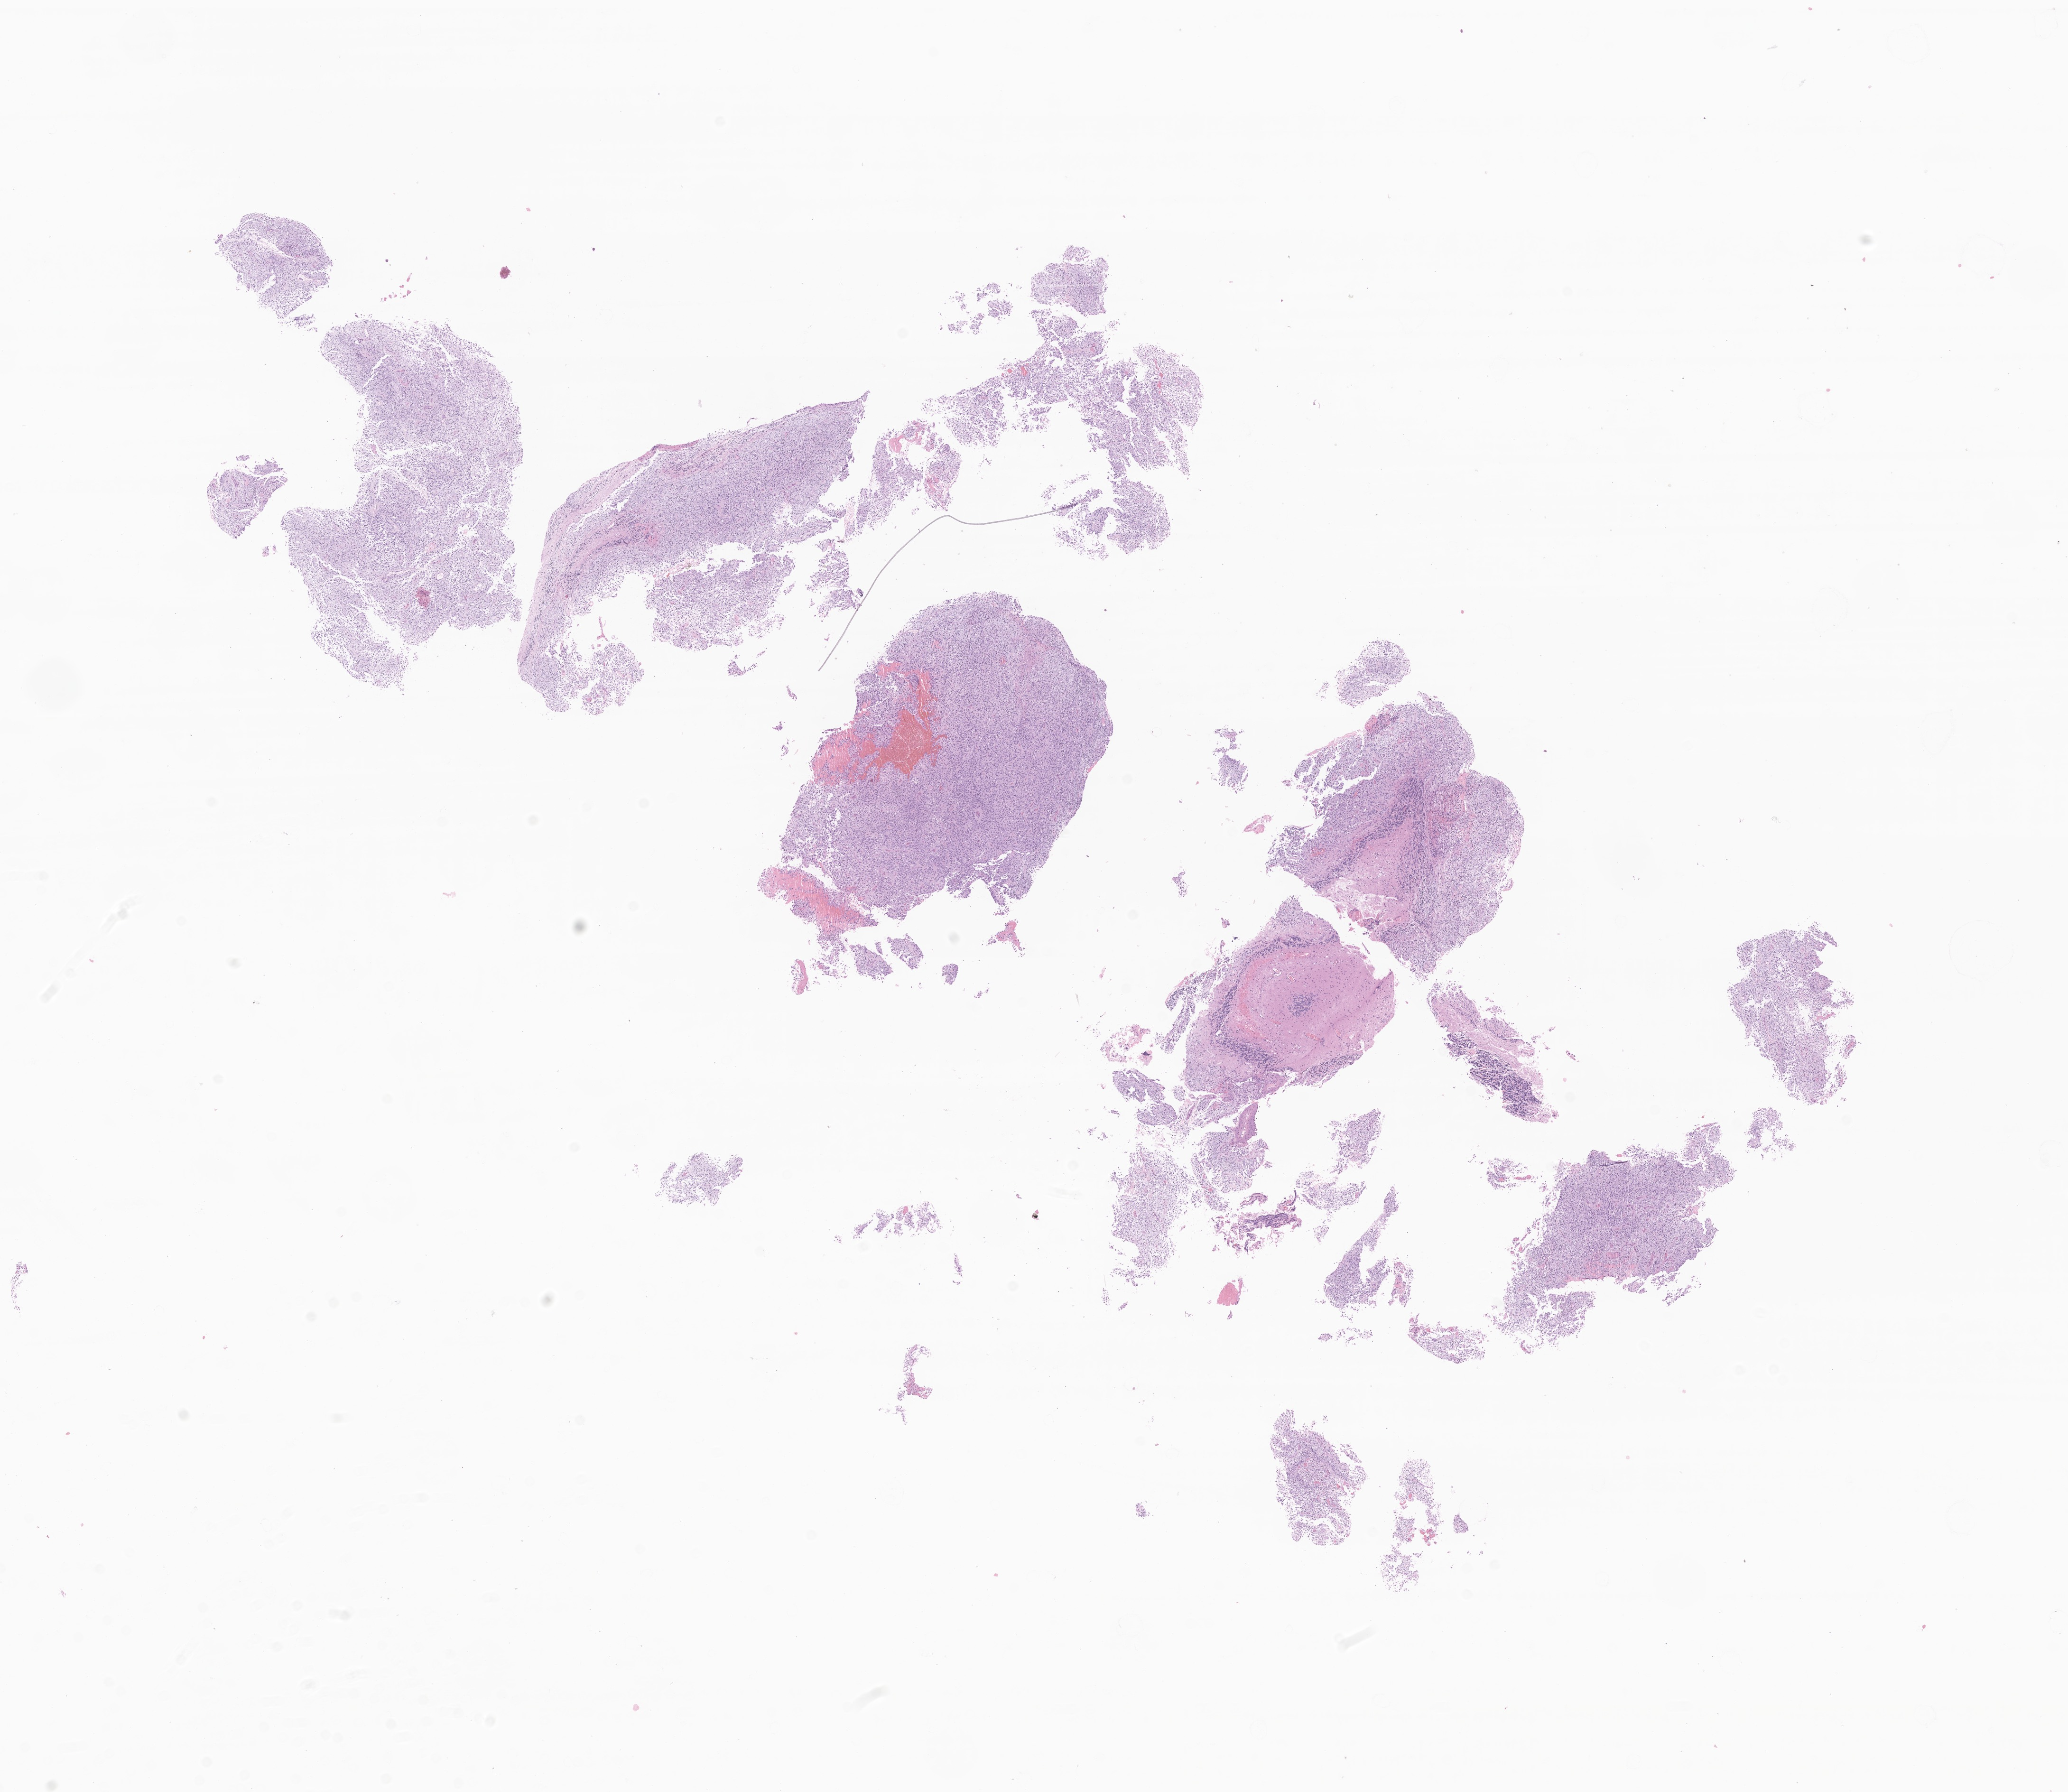
Hematoxylin and eosin (H&E) whole-slide image of tumor tissue from the brain — shown as a low-resolution overview of the whole scanned area (about 18.4 x 15.9 mm), formalin-fixed, paraffin-embedded (FFPE) tissue. Patient female; age 829 days (about 2.3 years).
Diagnosis (ICD-O-3 morphology term): Ependymoma, NOS.